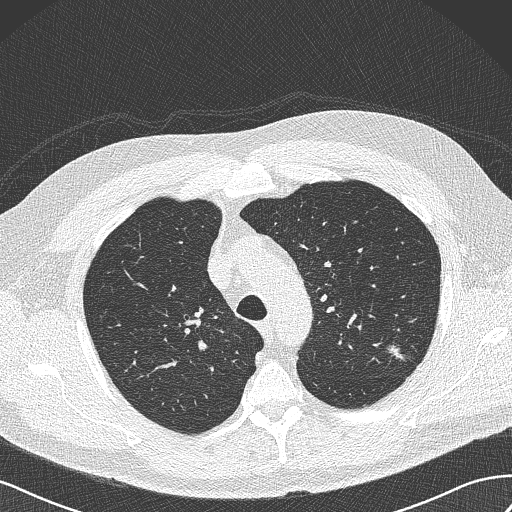
Chest CT (low-dose screening protocol), one axial image. Baseline screening round. Lung window (W 1500 / L -600 HU). 1 mm slice thickness. 120 kVp. Male, age 65 years at enrolment. Former smoker at enrolment.
Lesion marked by an expert reader, bounding box [x1, y1, x2, y2] px = [383, 341, 417, 372]. The screening reader recorded 3 non-calcified nodules or masses ≥4 mm on this exam (left upper lobe, left upper lobe, right upper lobe); which of them this box marks is not recorded.